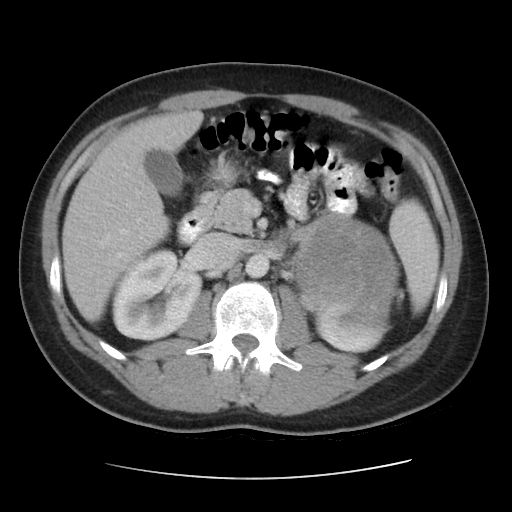
Contrast-enhanced abdominal CT, one axial slice. Slice 23 of 48 in the series (ordered by position). Intravenous contrast given. Soft-tissue window (W 400 / L 40 HU). 5 mm slice thickness. 512 × 512 image matrix, field of view 360 × 360 mm. Male patient, age 32 years. From the clinical record (not read from this slice): diagnosis: adrenocortical carcinoma; tumour side: left adrenal; tumour size at pathology: 14 cm; Ki-67 index: 67 %; stage (as recorded): 3.
Annotated regions visible in this slice (semi-automatically segmented with operator editing):
- mass: bounding box (x1, y1, x2, y2) in pixels: (299, 217, 395, 324)